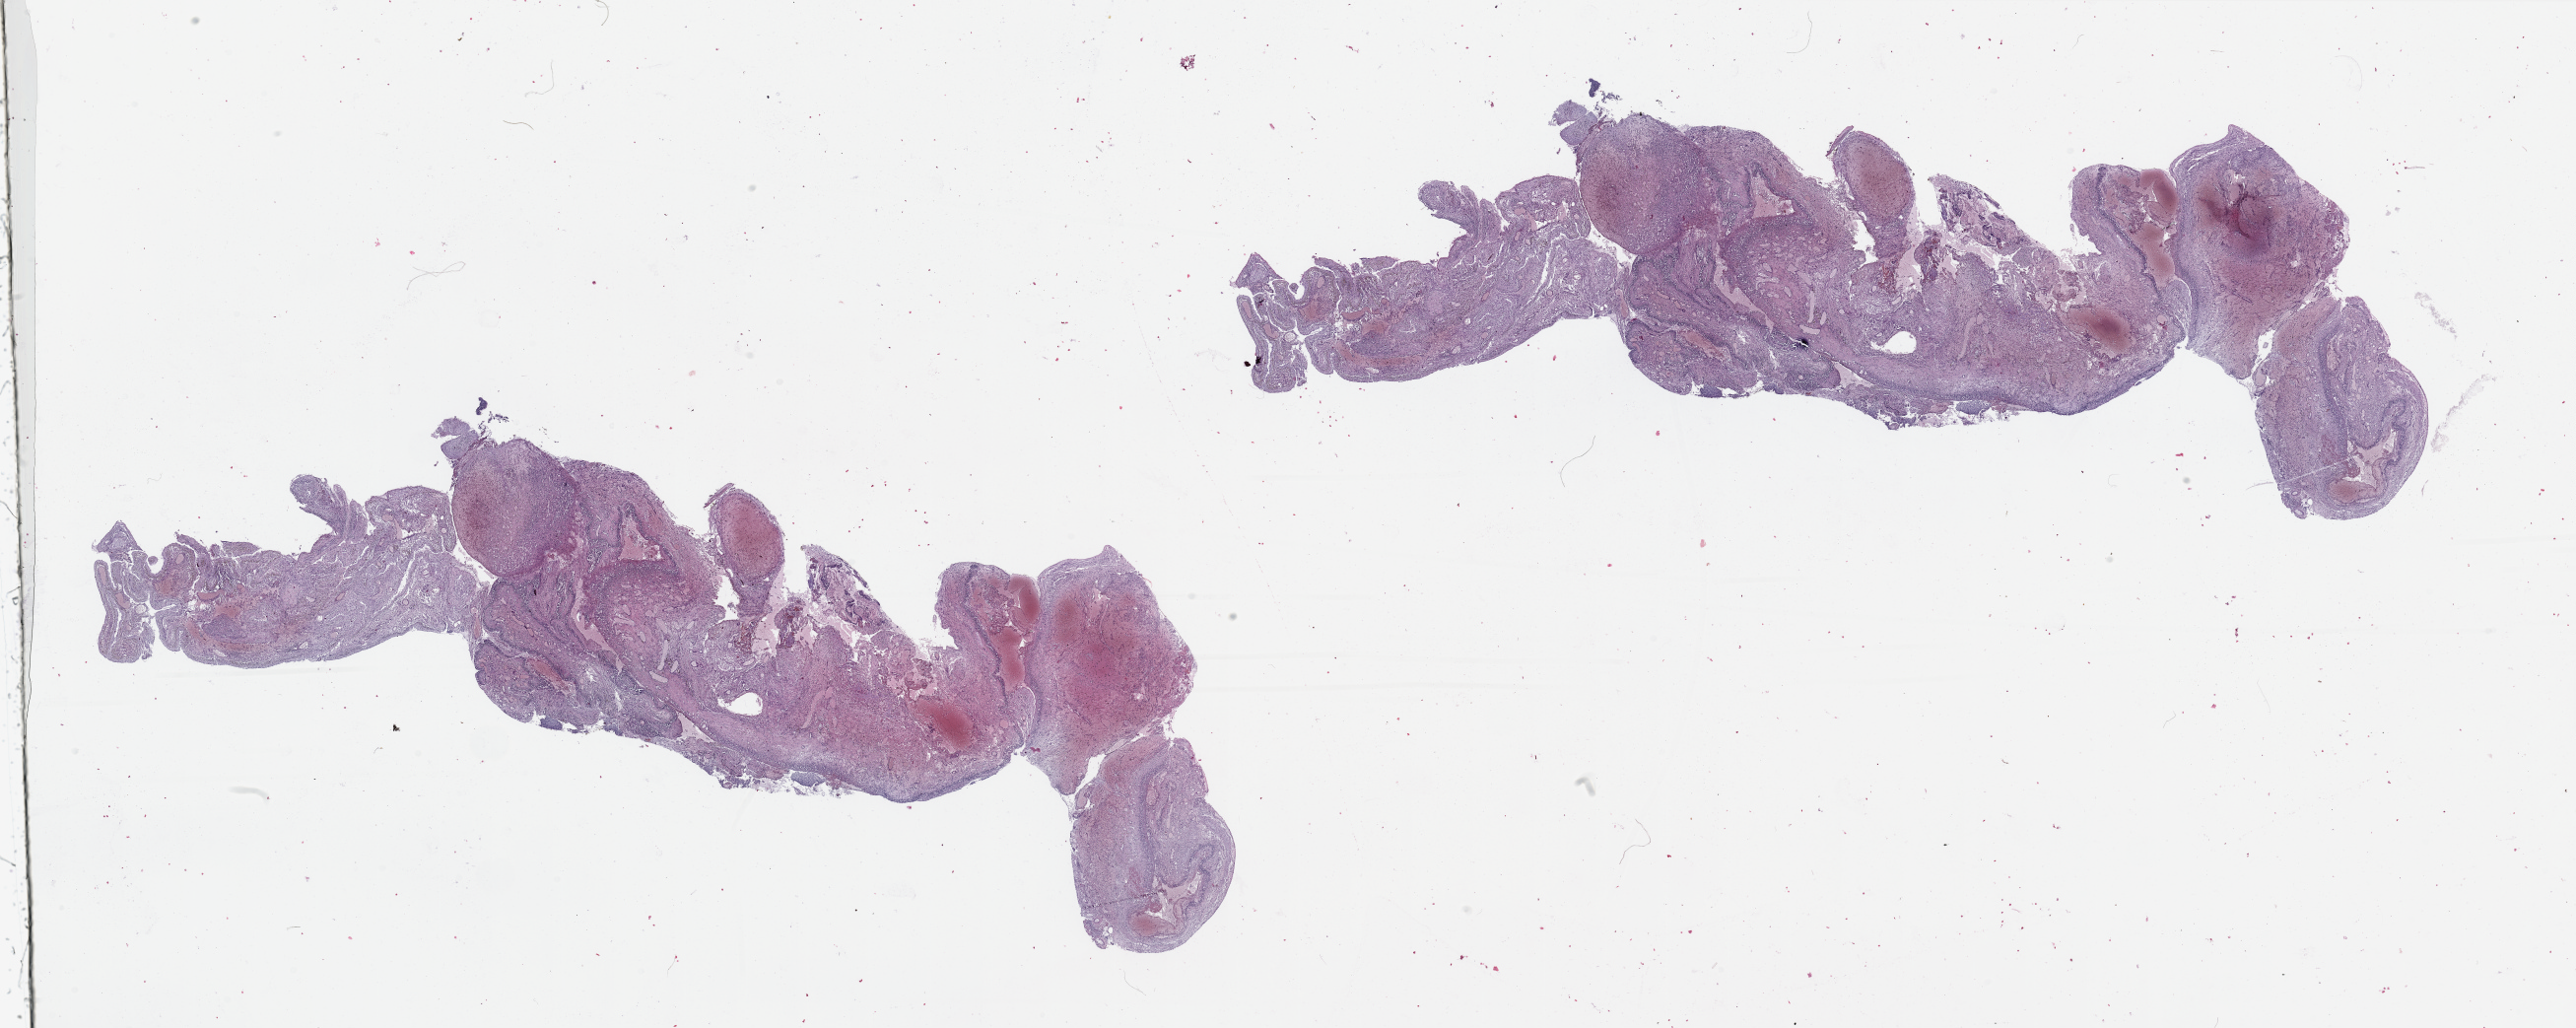
Whole-slide histology image, Hematoxylin and eosin (H&E) stained — whole scanned area (about 41.3 x 16.5 mm) shown as a low-resolution overview. Brain, tumour tissue. 40-year-old male patient.
Diagnosis: Glioblastoma. Primary tumour site (as recorded): parietal lobe.